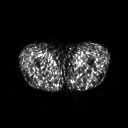
FDG PET of an extremity soft-tissue mass (from a PET/CT study), one axial slice; position 261 of 311 along the scan axis; 3.27 mm slice thickness; 128 × 128 image matrix. Male patient, age 29 years. Case-level facts recorded for this patient, not image findings: histological type: mixoid liposarcoma; grade: low; site of the primary tumour: left thigh.
Annotated regions visible in this slice (expert contour drawn on MRI and transferred to this co-registered scan by the dataset authors):
- gross tumour volume (mass): box from (x=74, y=57) to (x=81, y=65) px